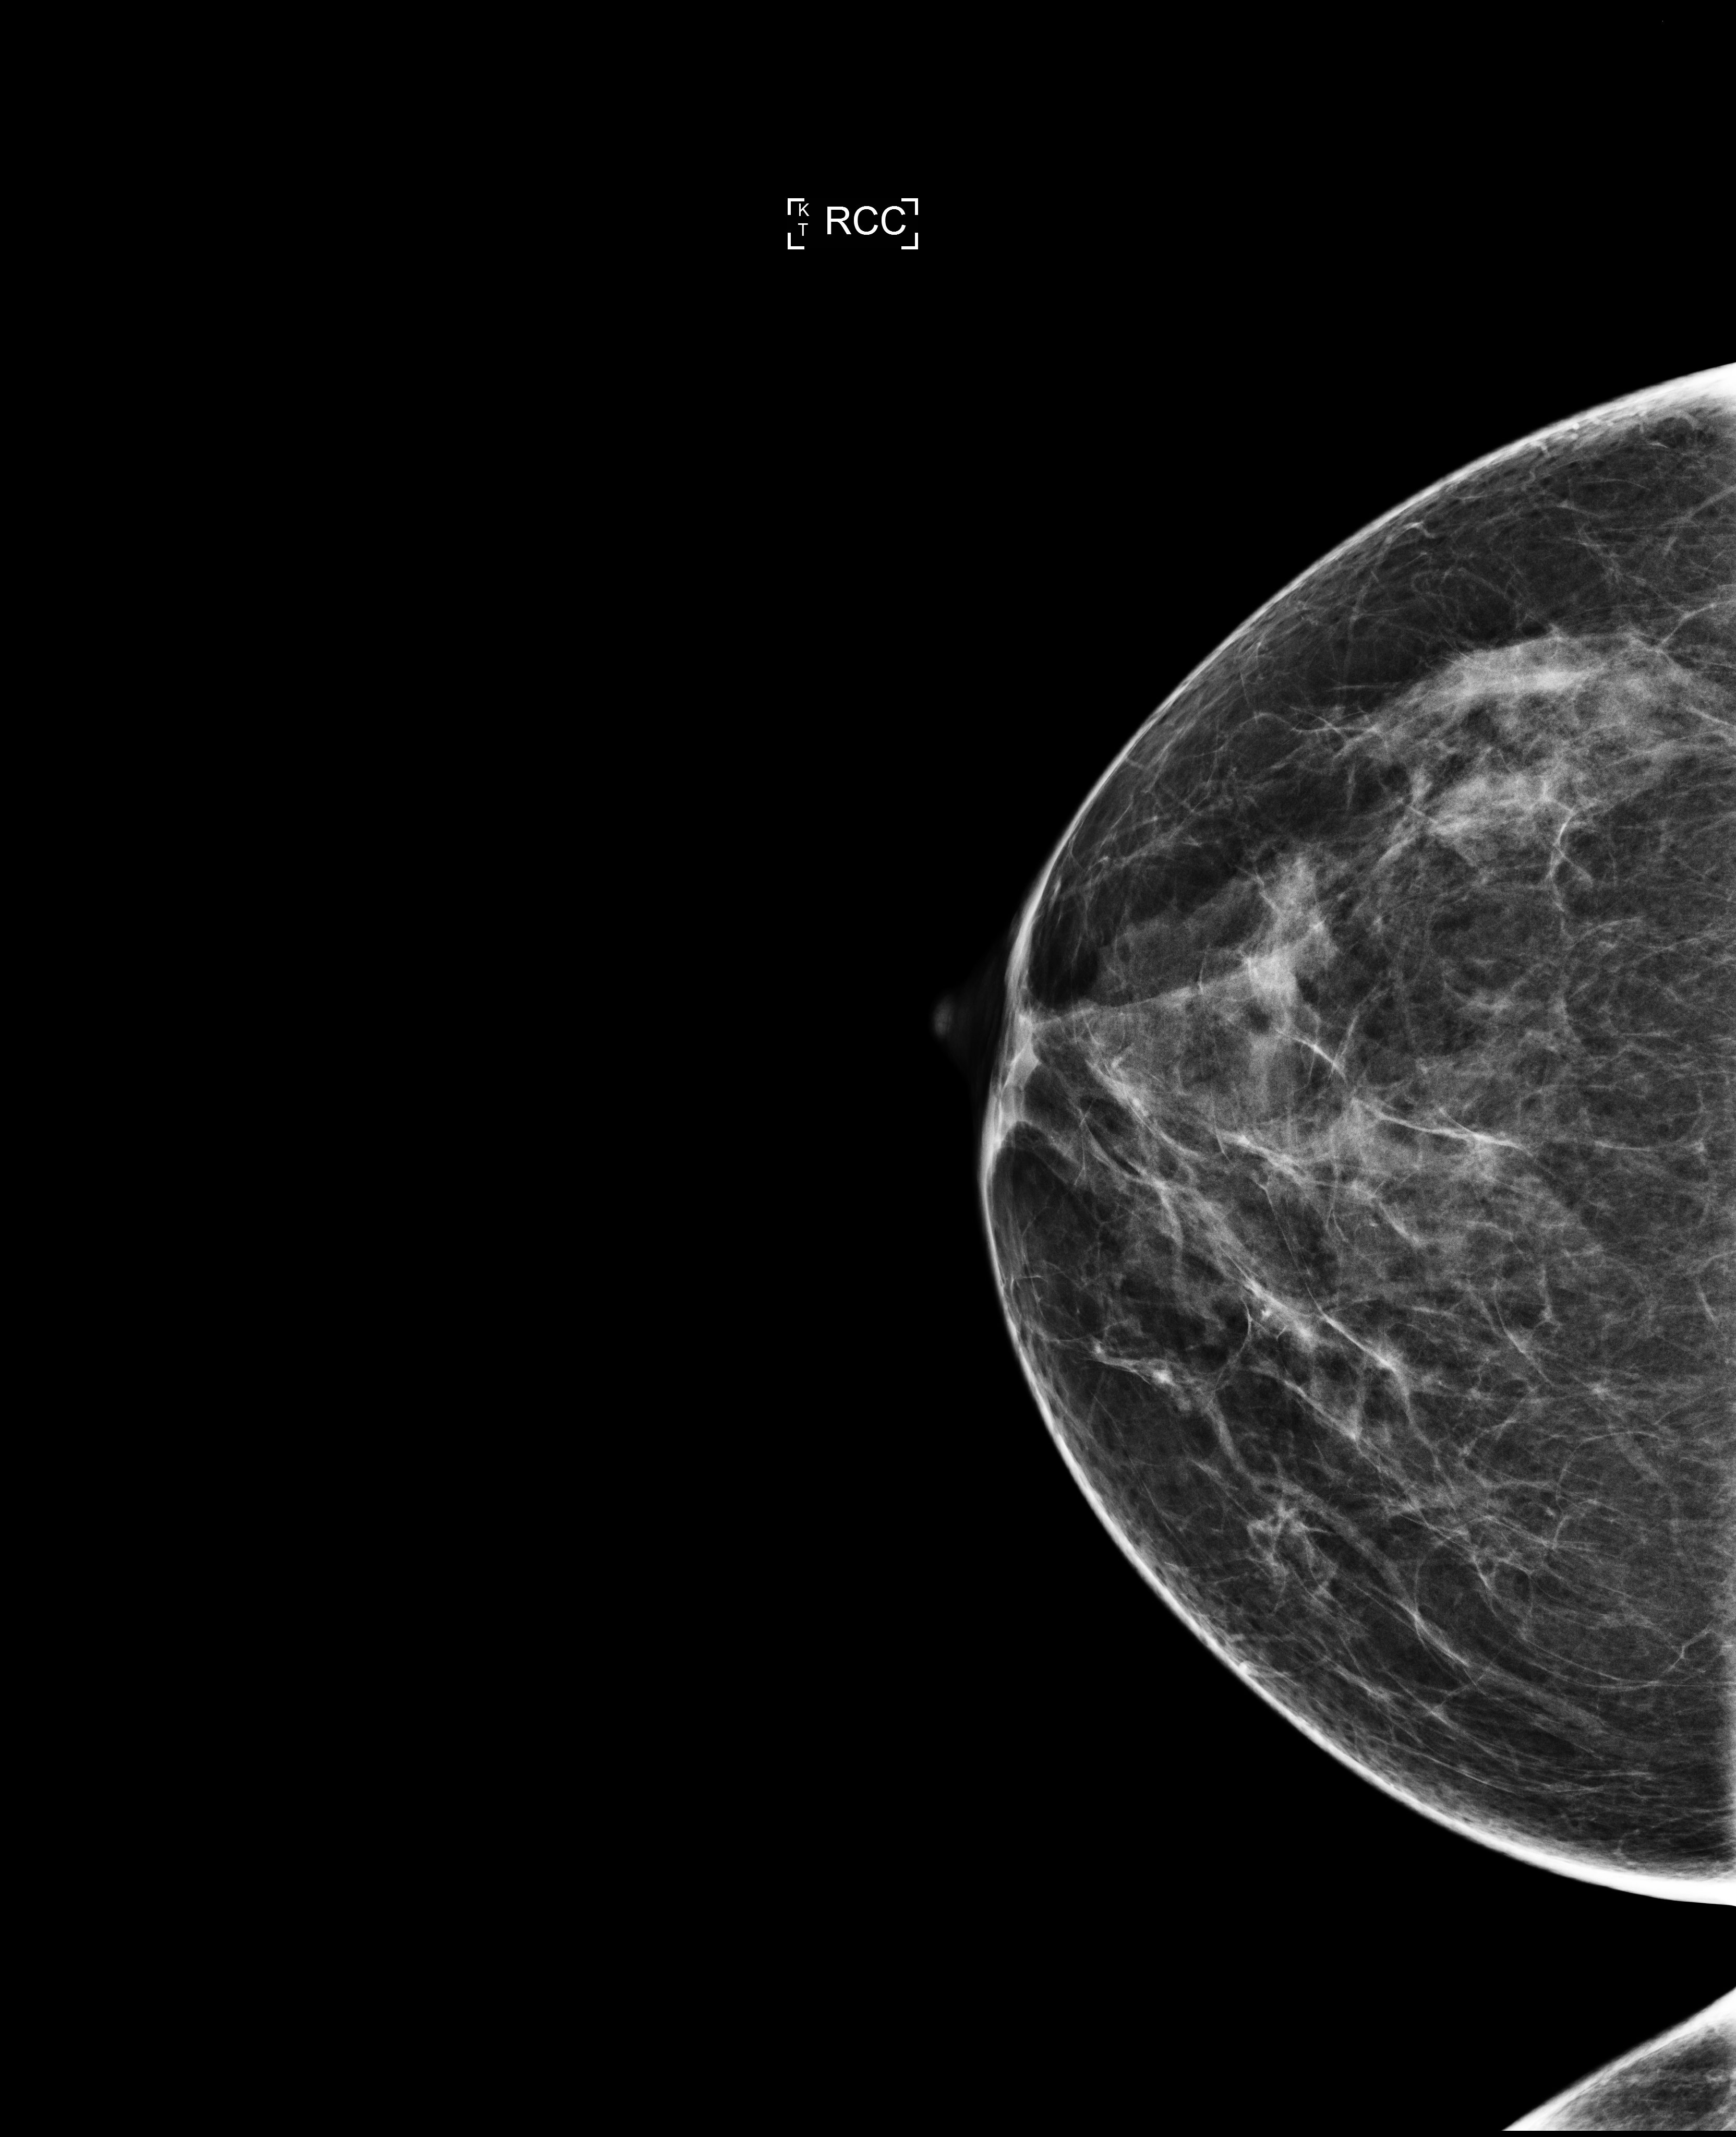
Screening examination; compressed breast thickness 65 mm. Female patient, age 54 years.
Image type: full-field digital mammogram. Breast: right. Projection: craniocaudal (CC) view.